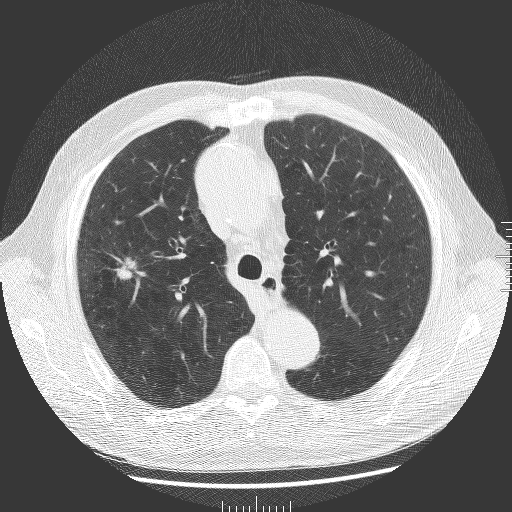
Low-dose screening chest CT, one axial slice; position 131 of 181 along the scan axis; lung window (W 1500 / L -600 HU); 2 mm slice thickness; 512 × 512 image matrix, field of view 380 × 380 mm.
Annotated regions visible in this slice (manually delineated by an expert):
- lesion 1 (tumor, upper lobe of right lung): bounding box <116,258,136,280> (left, top, right, bottom; pixels)